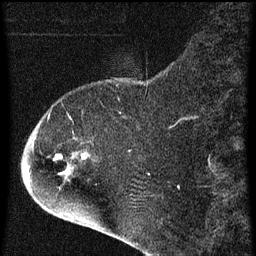
Breast MRI (dynamic contrast-enhanced), one sagittal slice. Dynamic contrast-enhanced series, image 2 of 4 at this slice position (ordered by acquisition). 1.5 T. TE 4.2 ms, TR 8 ms. 256 × 256 image matrix. Patient: female, 71 years.
Structures marked on this image (semi-automatically segmented with operator editing):
- analysis volume of interest (the breast-tissue region the enhancement analysis was run in; not a lesion): box from (x=32, y=96) to (x=140, y=205) px
- tumour enhancement mask (voxels above the 70 % enhancement threshold inside the analysis volume of interest): (x=54, y=154)–(x=87, y=161)